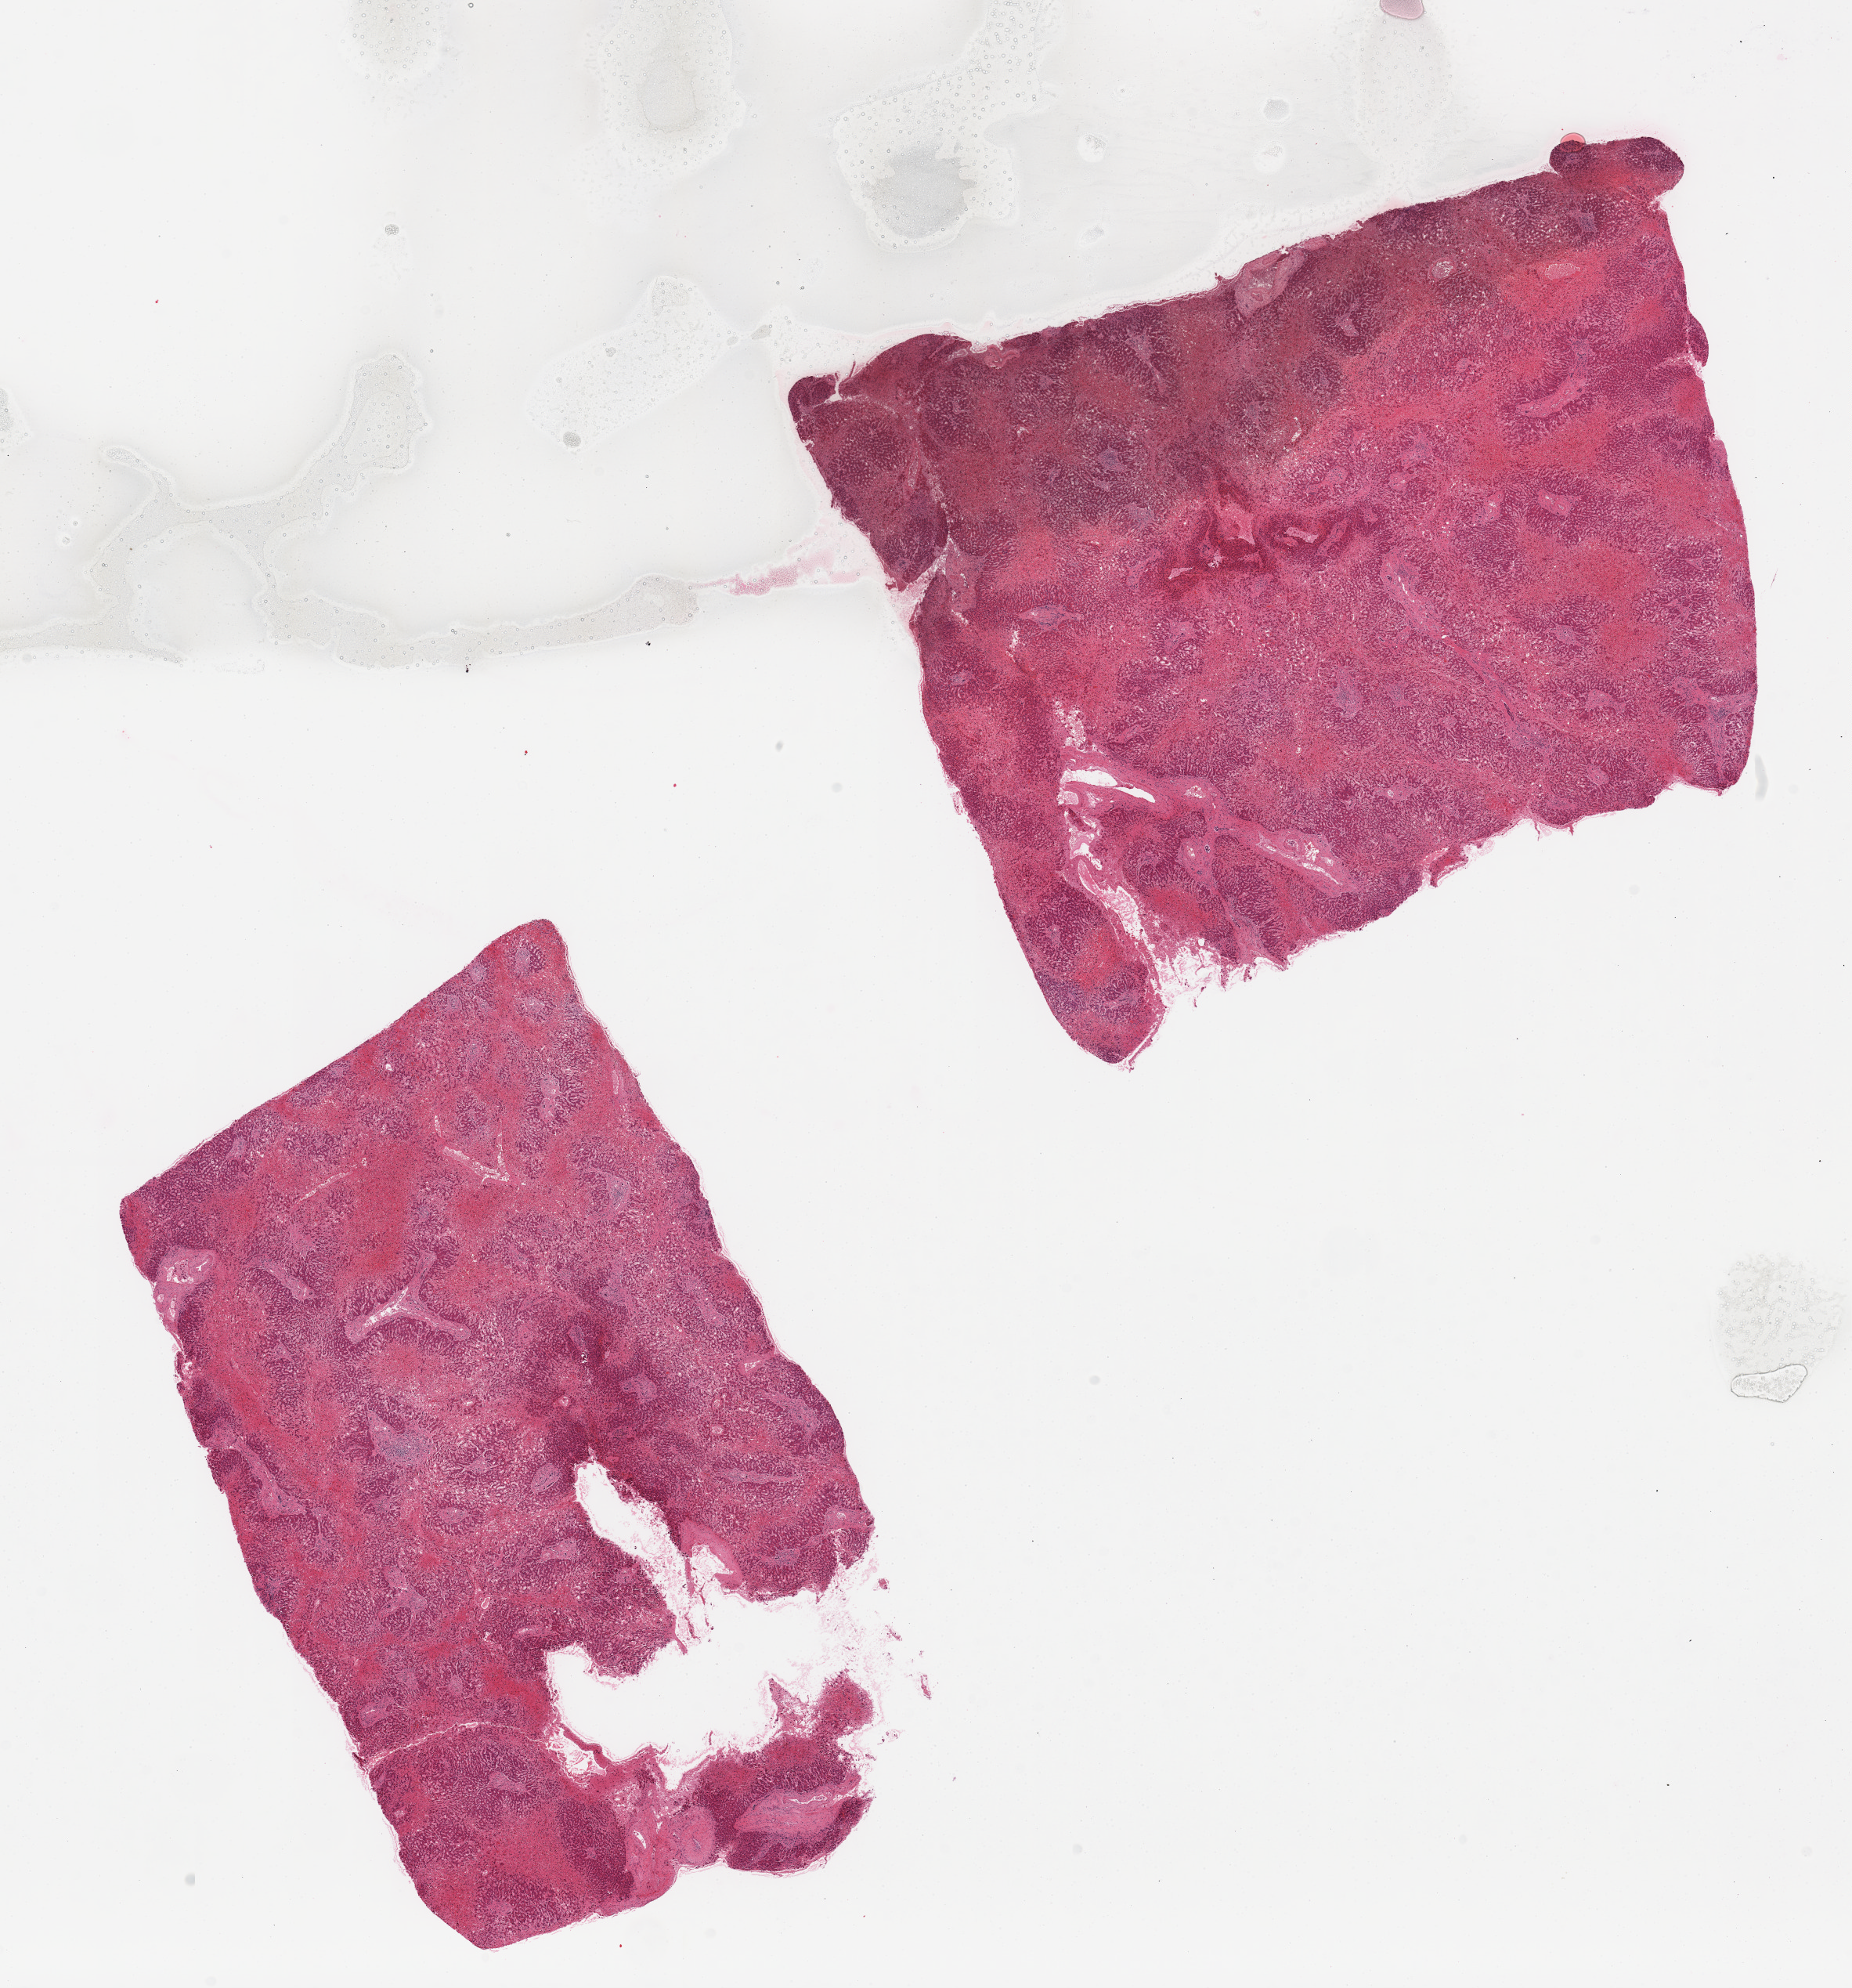
Digitized hematoxylin and eosin (H&E)-stained section, whole scanned area (about 18.7 x 20.1 mm) shown as a low-resolution overview; PAXgene-fixed paraffin-embedded (PFPE) section; target tissue: liver; tissue donor sample.
• review note (as recorded): 2 pieces; severe central vascular congestion with liver cell atrophy [c/w heart failure]; only thin rim of periportal liver cells remain intact